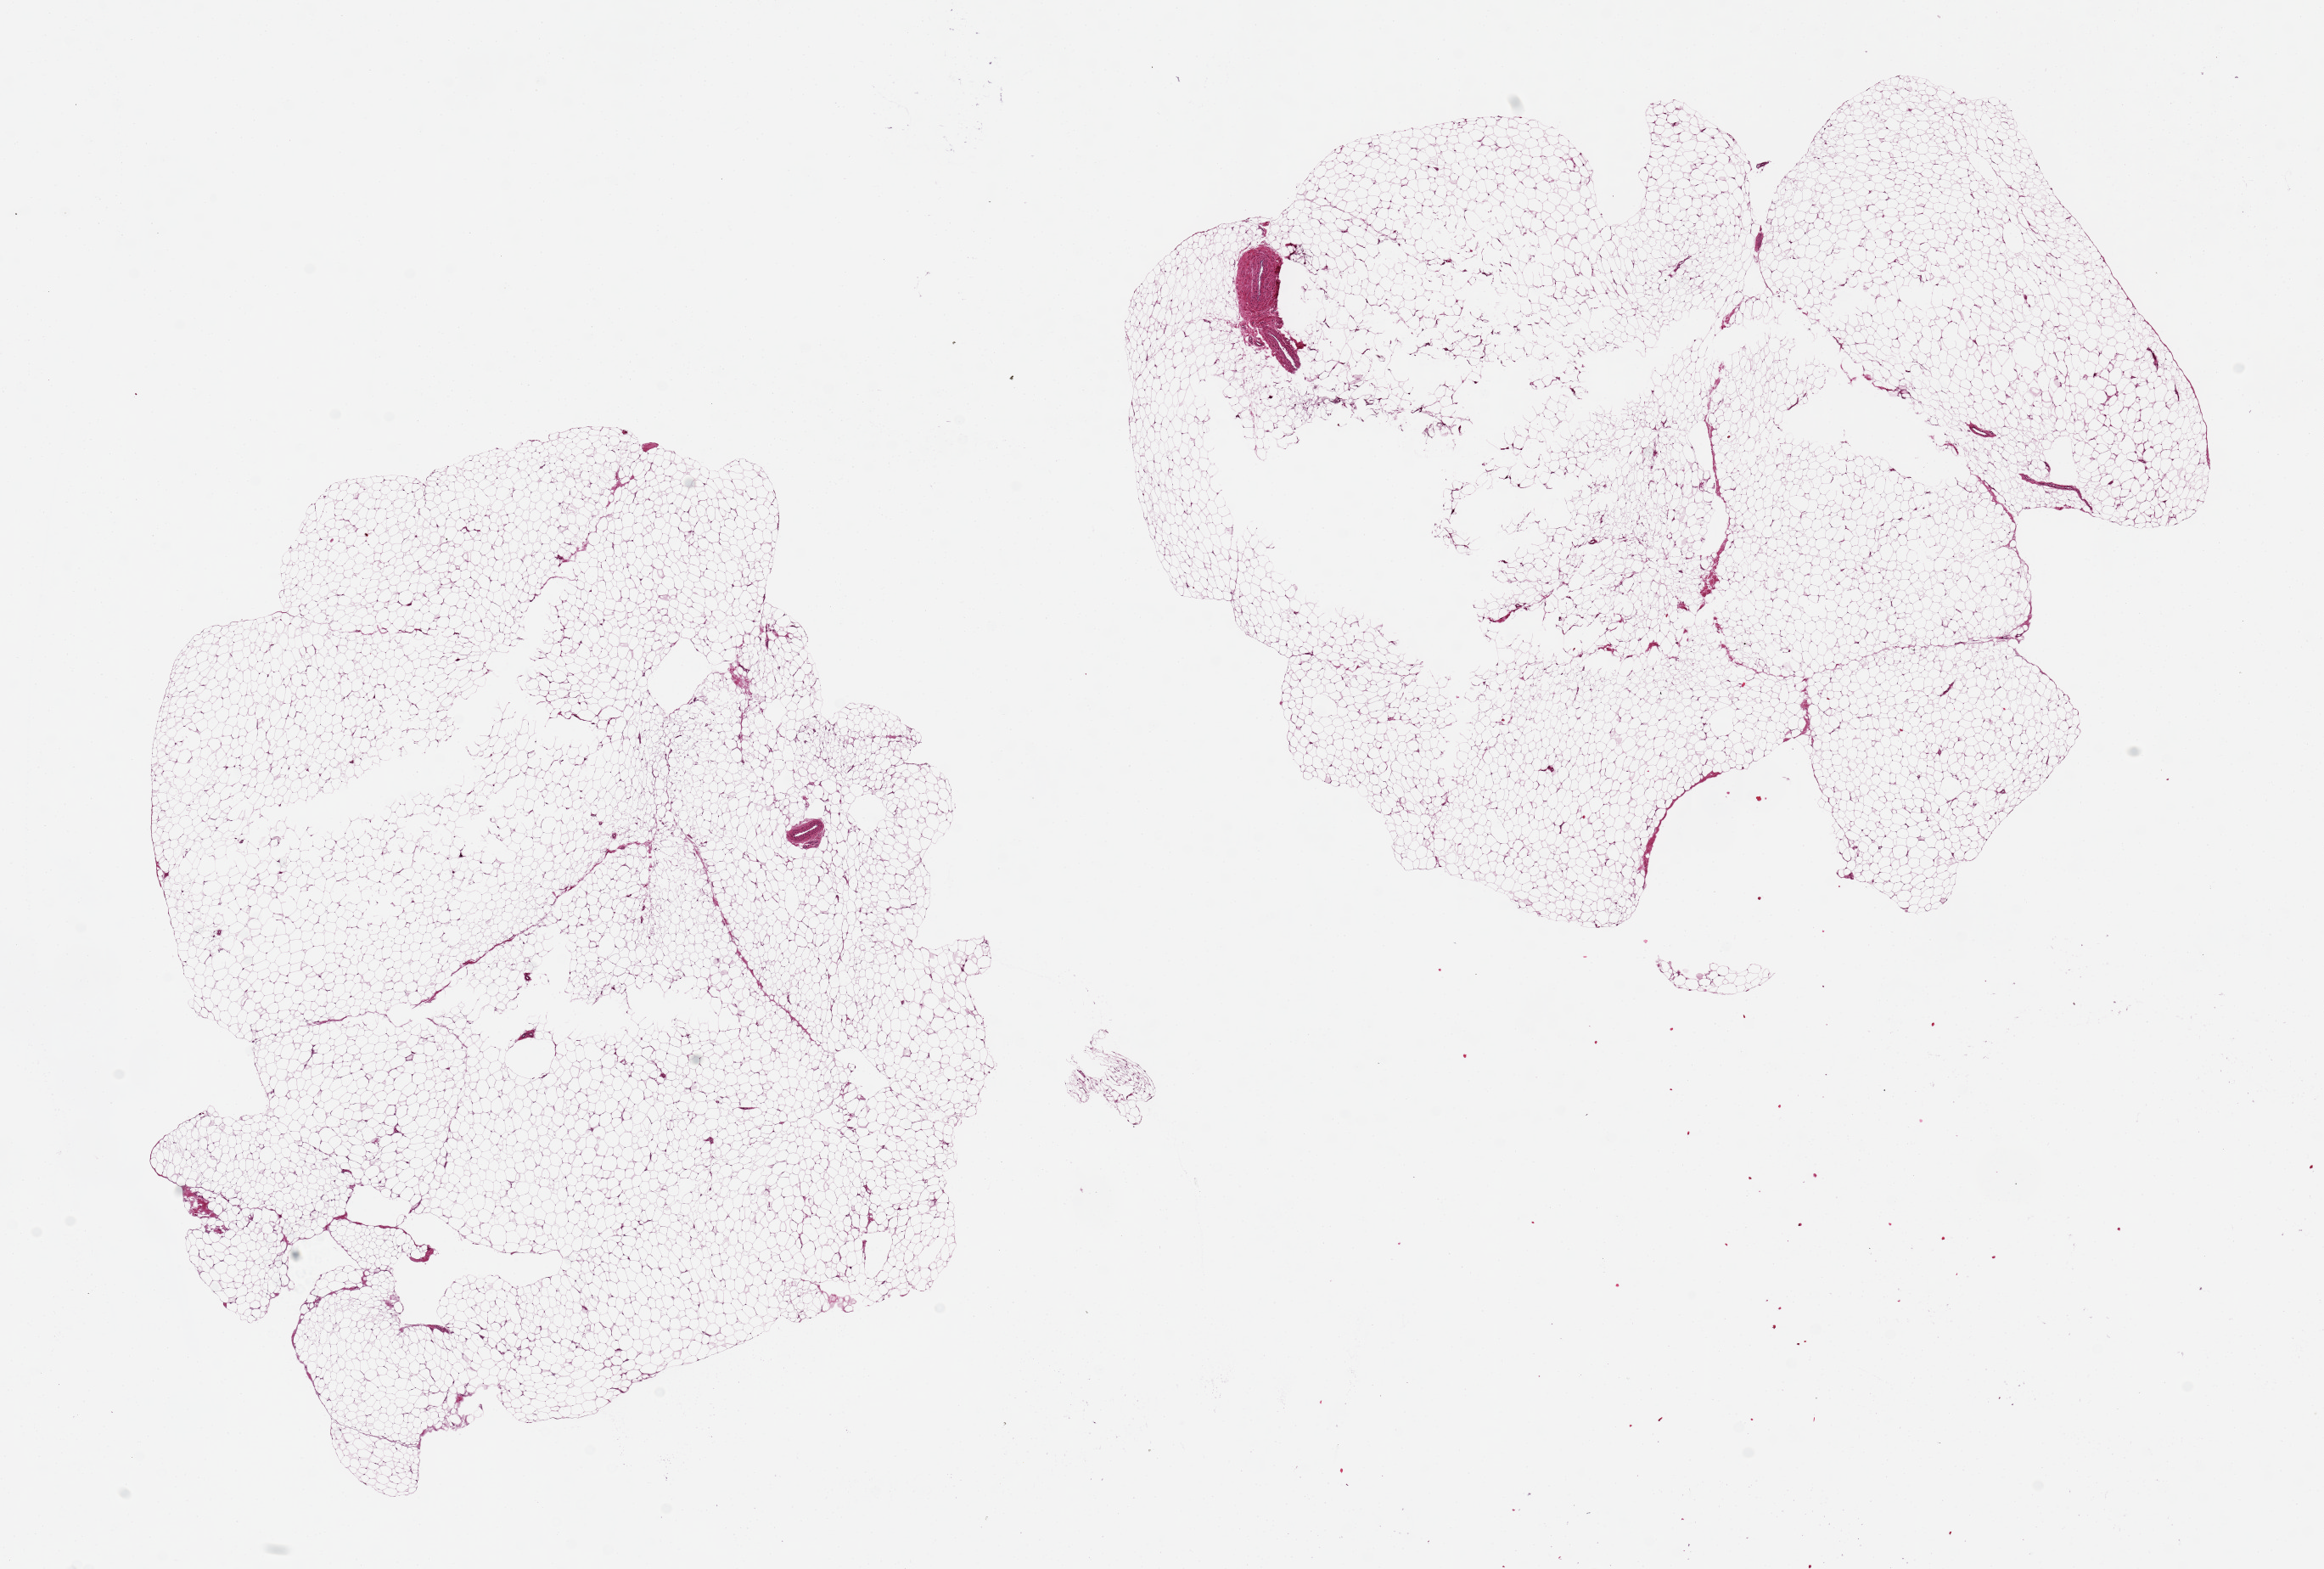
H&E whole-slide image, brightfield — a low-resolution overview of the entire scanned area, about 21.7 x 14.6 mm. PAXgene-fixed paraffin-embedded (PFPE) section. Sampled site (target tissue): adipose tissue. Donor tissue sample. Male donor.
Reviewer comment on this tissue sample: 2 pieces, 9x8 & 8x7 mm; small focal hole of unfixed tissue, 2.6x2 mm.